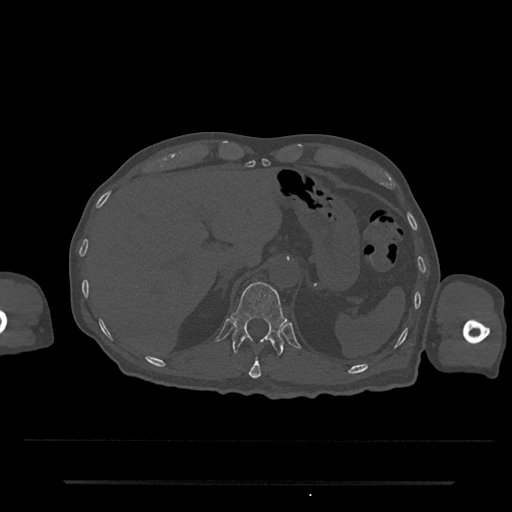
CT including the spine, one axial slice; slice 212 of 797 in the series (ordered by position); 120 kVp; bone window (W 1800 / L 400 HU); 0.5 mm slice thickness; 512 × 512 image matrix, field of view 427 × 427 mm. Male patient, age 74 years. Case-level facts recorded for this patient, not image findings: primary cancer: prostate.
Structures marked on this image (semi-automatic segmentation, software-assisted and operator-edited):
- T11 vertebra: bounding box (x1, y1, x2, y2) in pixels: (249, 358, 261, 379)
- T12 vertebra: (231, 281, 287, 355)